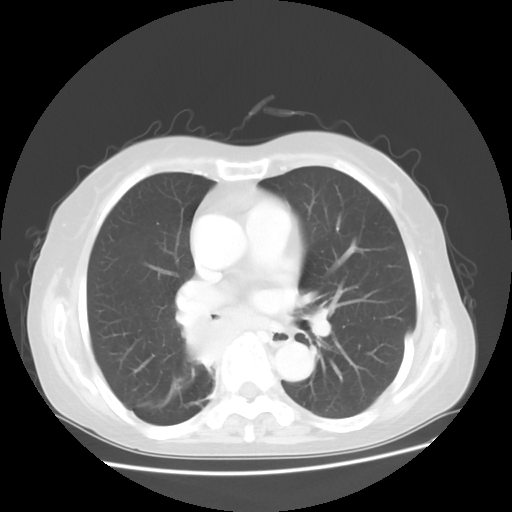
Chest CT, one axial slice; slice 25 of 48 in the series (ordered by position); reconstruction kernel STANDARD; lung window (W 1500 / L -600 HU); 5 mm slice thickness; 512 × 512 image matrix. Patient: female, 63 years. From the clinical record (not read from this slice): clinical TNM (as recorded): T2 N3 M1b.
Annotated regions visible in this slice (bounding box drawn by a radiologist):
- lung tumour (recorded histology: small cell carcinoma): box from (x=176, y=309) to (x=222, y=372) px